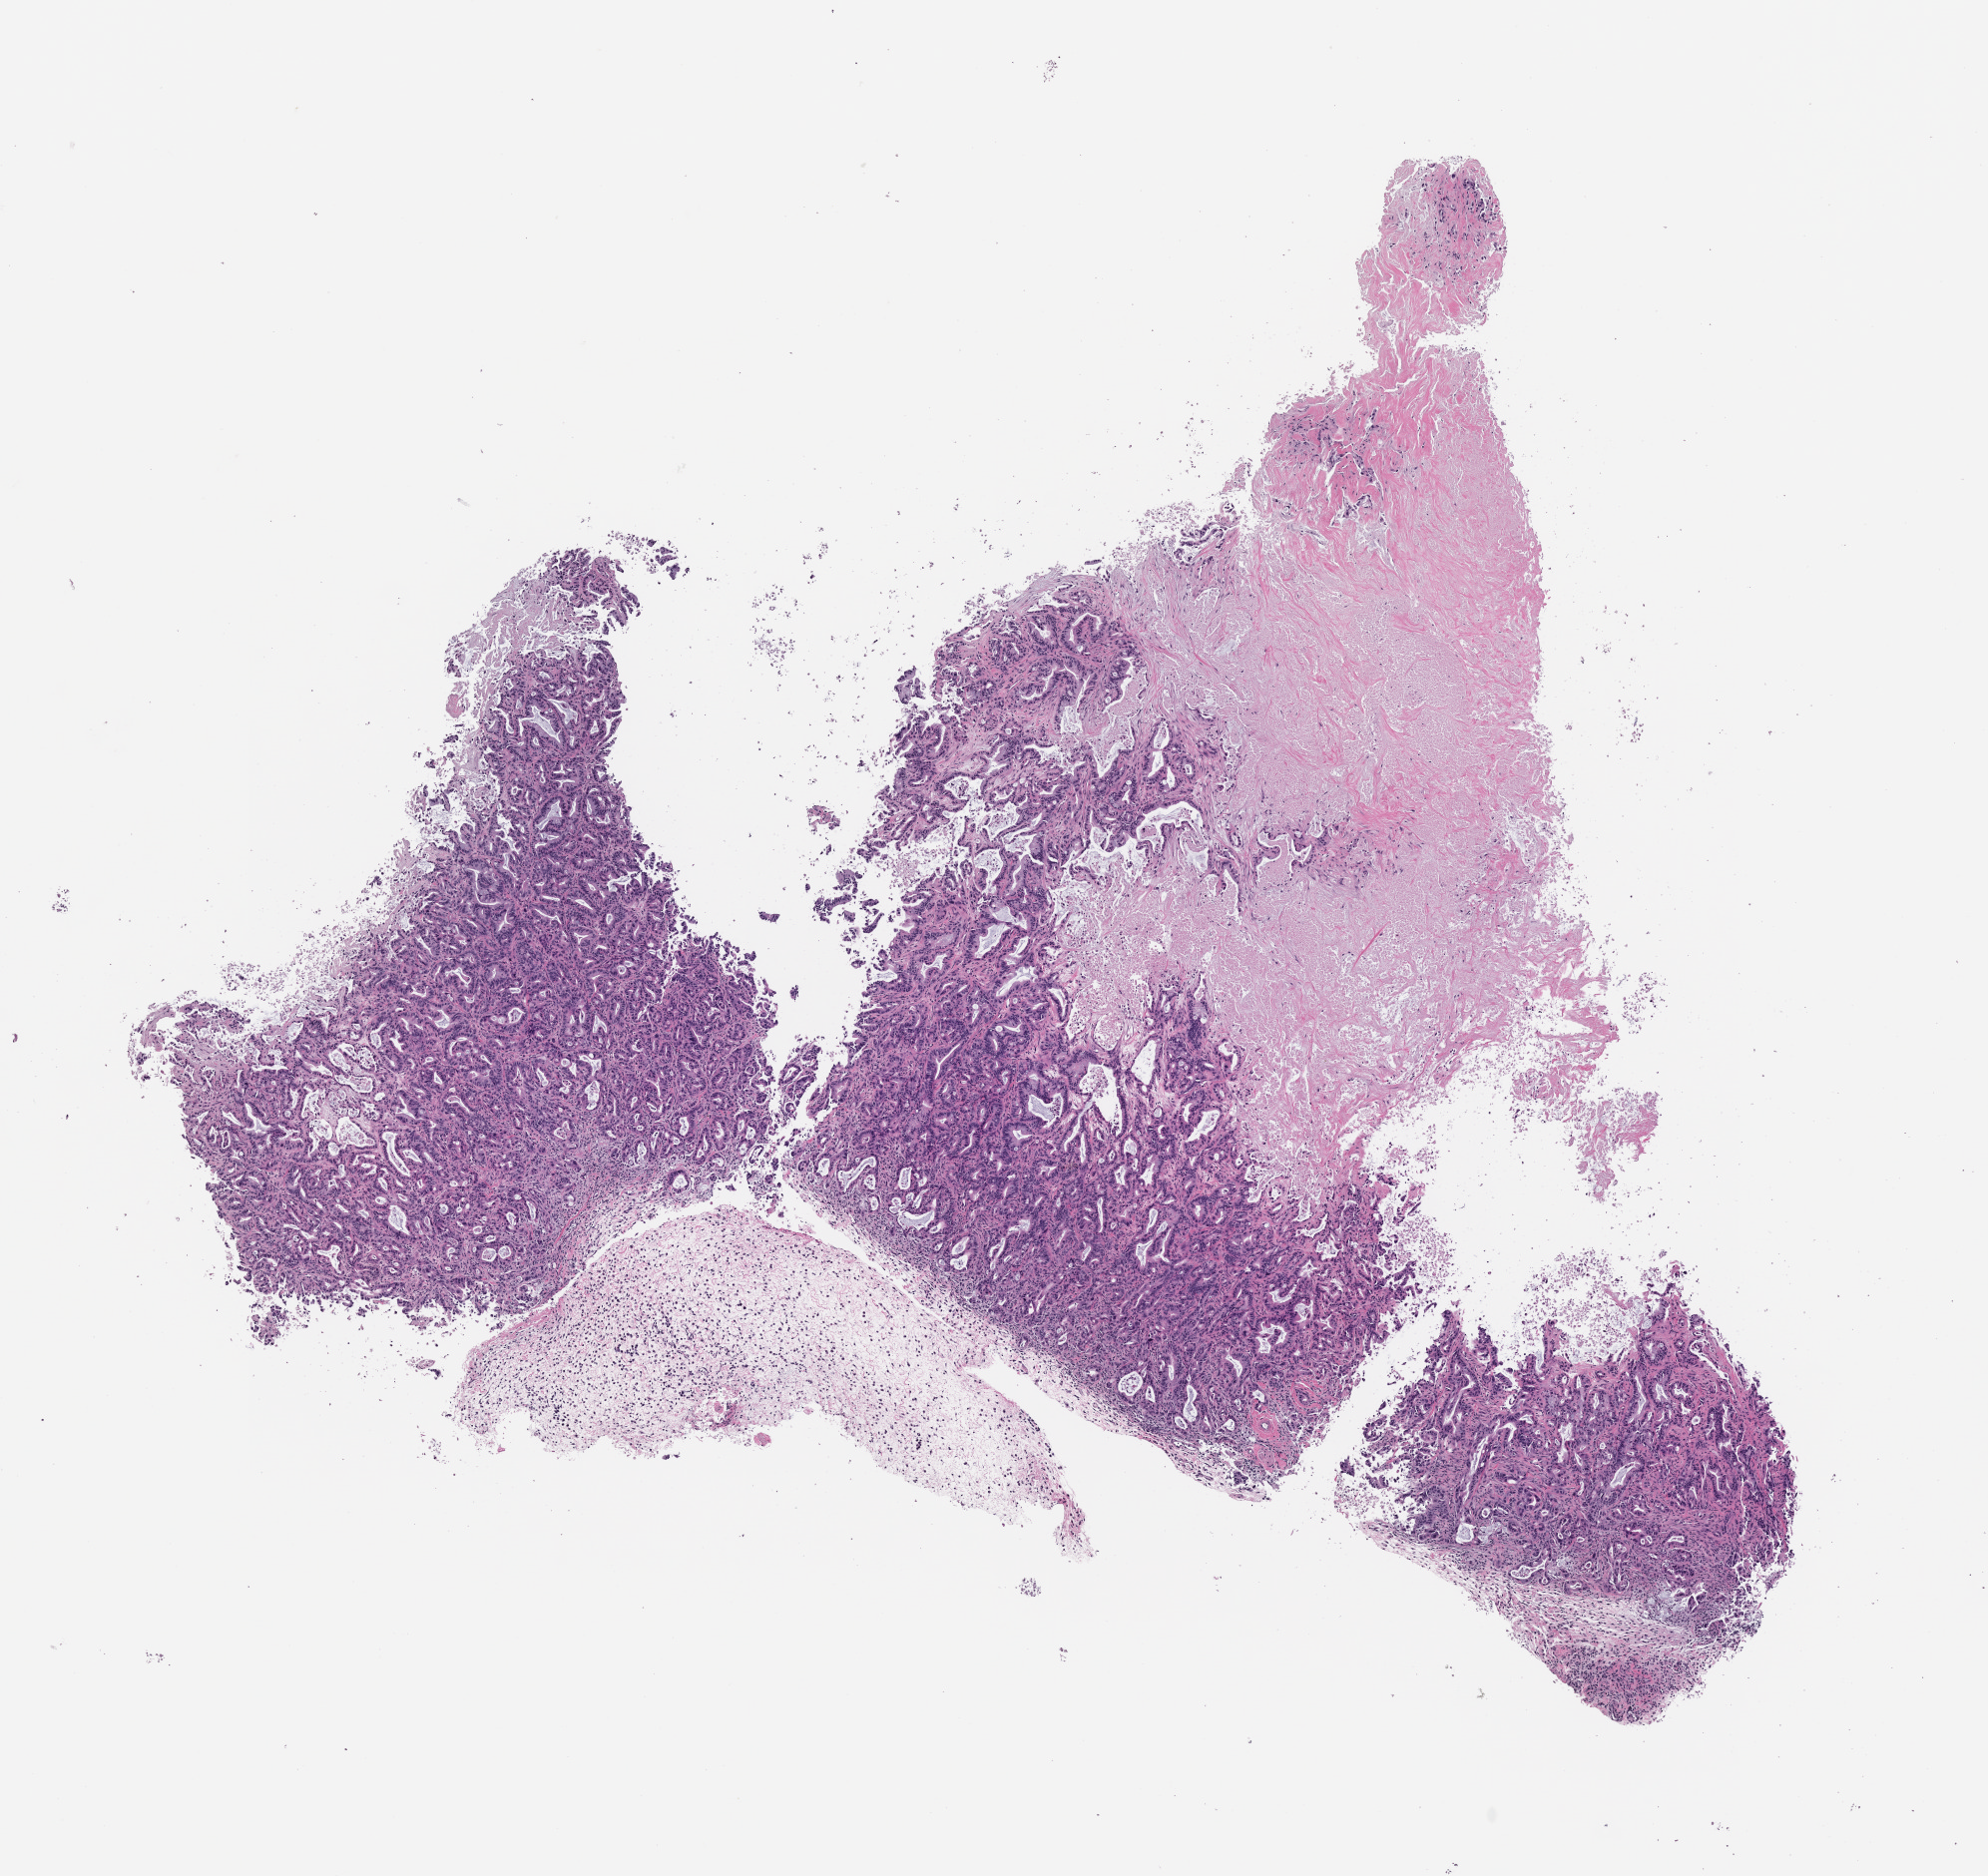
Whole-slide image, H&E: patient-derived xenograft (human tumor grown in a mouse), passage 7 — low-resolution overview of the scanned area, about 8.0 x 7.6 mm. FFPE section. Originating tumor site category: pancreas.
- originating patient diagnosis: Pancreatic Adenocarcinoma